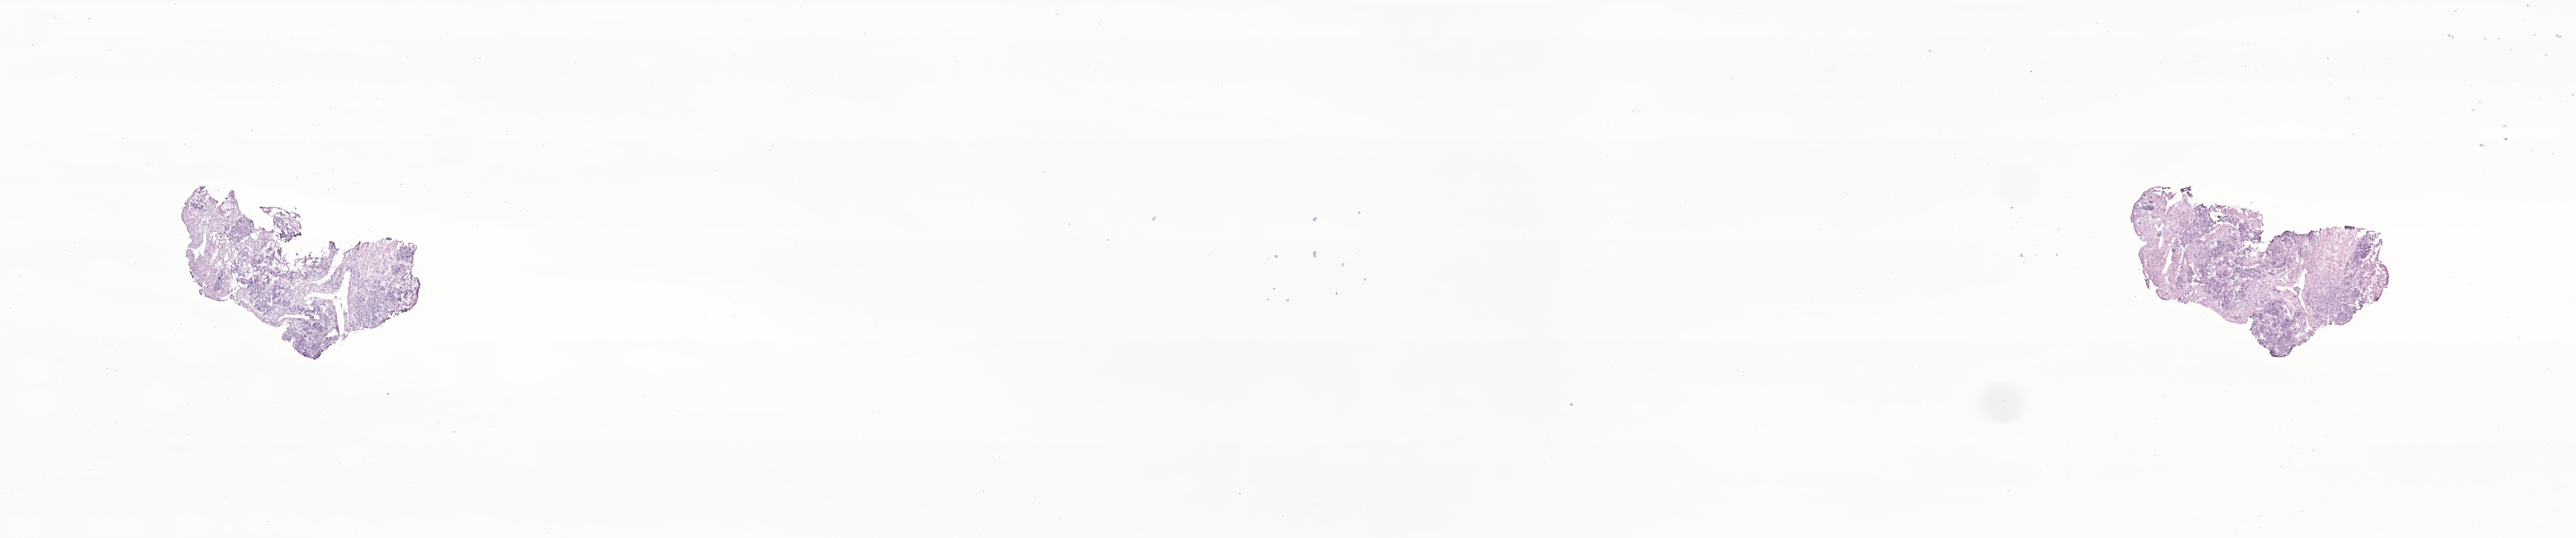
Digitized hematoxylin and eosin (H&E)-stained section of tumor tissue from the head and neck, low-resolution overview of the scanned area, about 27.3 x 5.7 mm, frozen section. Patient male; age 38 months (3 years 2 months).
- diagnosis (ICD-O-3 morphology term): Alveolar rhabdomyosarcoma